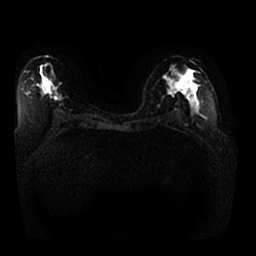
Breast MRI, one axial slice. Slice 13 of 25 in the series (ordered by position). Diffusion-weighted series; image 2 of 4 stored at this slice position (different b-values; order by instance number). 1.5 T. 256 × 256 image matrix. Female patient.
Structures marked on this image (manually delineated by an expert):
- tumour on diffusion-weighted imaging: box from (x=177, y=80) to (x=185, y=90) px